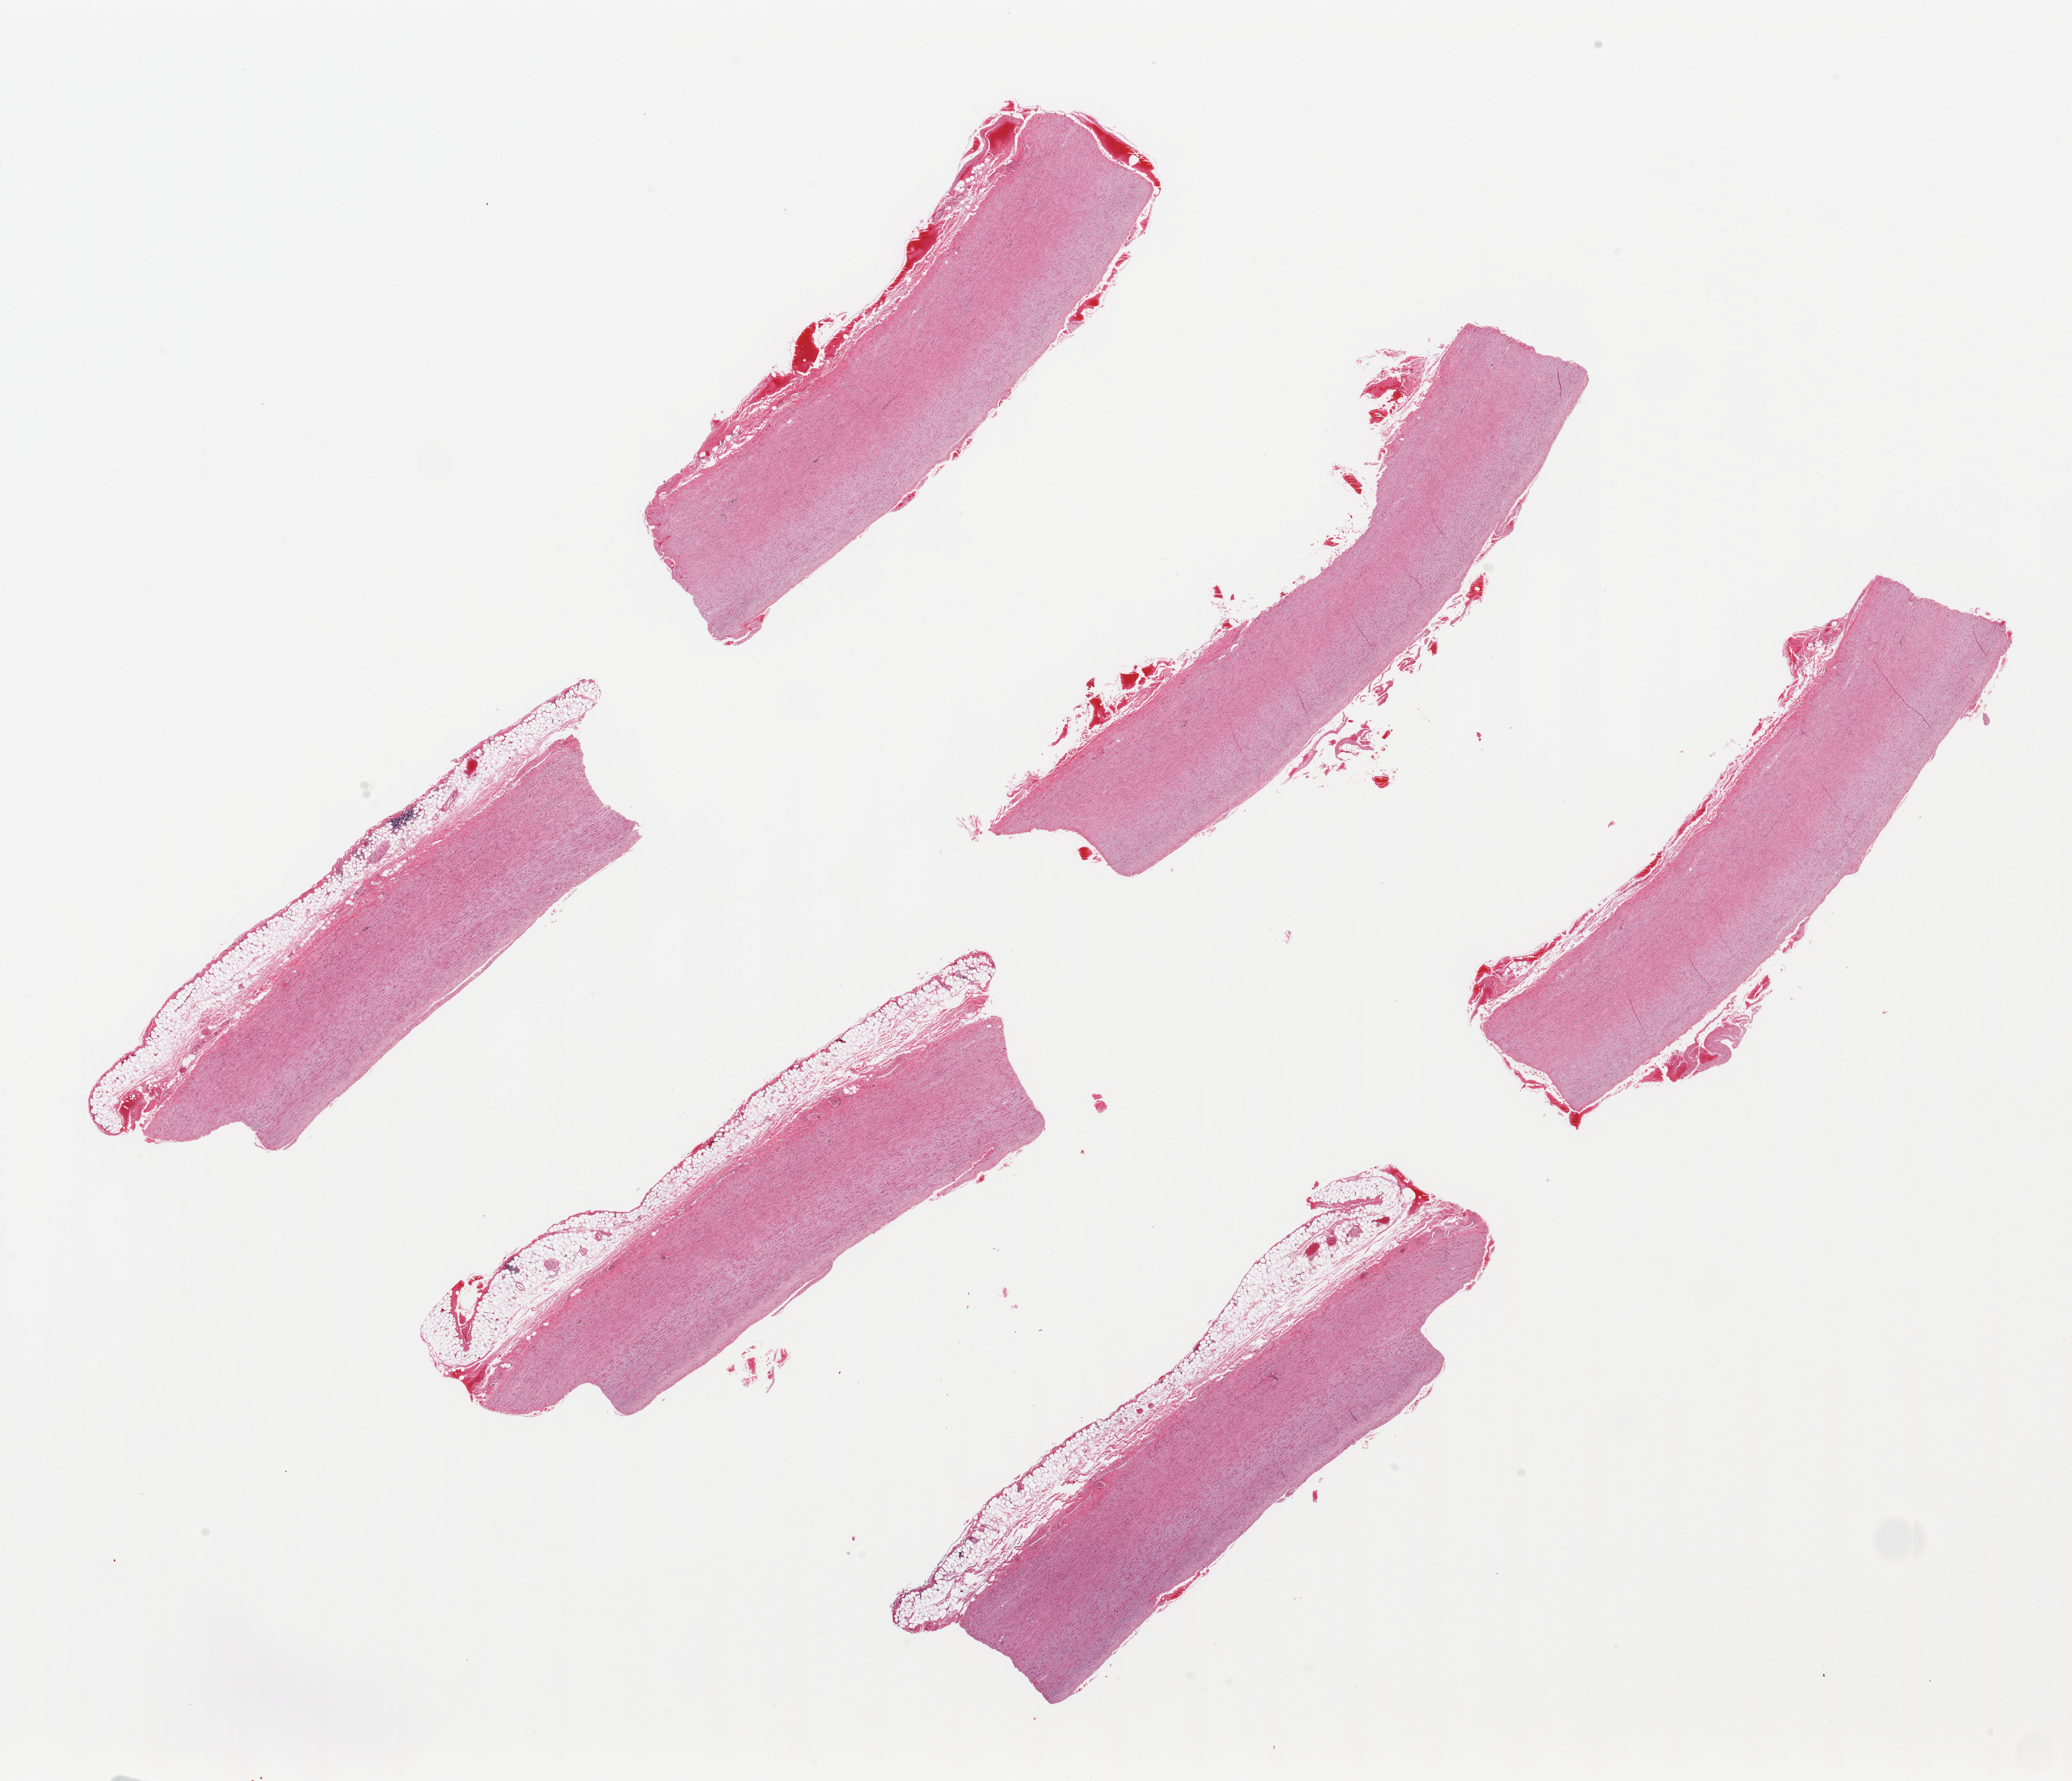
Hematoxylin and eosin (H&E) whole-slide image, brightfield, whole scanned area (about 25.6 x 22.0 mm) shown as a low-resolution overview. PAXgene-fixed paraffin-embedded (PFPE) section. Target tissue: aorta. Tissue donor sample. Donor sex: male.
Reviewer comment on this tissue sample: 6 pieces up to 8x2 mm.